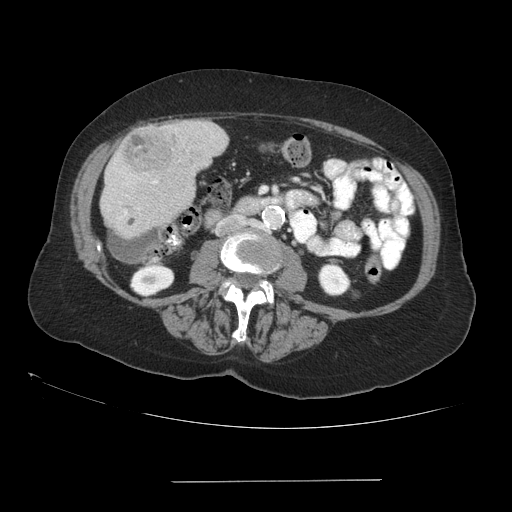
Contrast-enhanced abdominal CT (liver protocol), one axial slice. Slice 25 of 89 in the series (ordered by position). Reconstruction kernel STANDARD. 140 kVp. Soft-tissue window (W 400 / L 40 HU). 2.5 mm slice thickness. 512 × 512 image matrix, field of view 400 × 400 mm. Case-level facts recorded for this patient, not image findings: diagnosis: hepatocellular carcinoma (patient treated with transarterial chemoembolisation; whether this scan precedes or follows treatment is not stated here); TNM stage (as recorded): Stage-IVA; Child-Pugh class: A; tumour differentiation: poorly differentiated; tumour nodularity: uninodular.
Outlined on this slice (semi-automatic segmentation, software-assisted and operator-edited):
- liver parenchyma outside the tumour (the mass and vessels are separate outlines, so this box may not span the whole liver): bounding box (x1, y1, x2, y2) in pixels: (100, 120, 228, 239)
- mass: (123, 129, 171, 173)
- liver vessels: (124, 181, 157, 214)